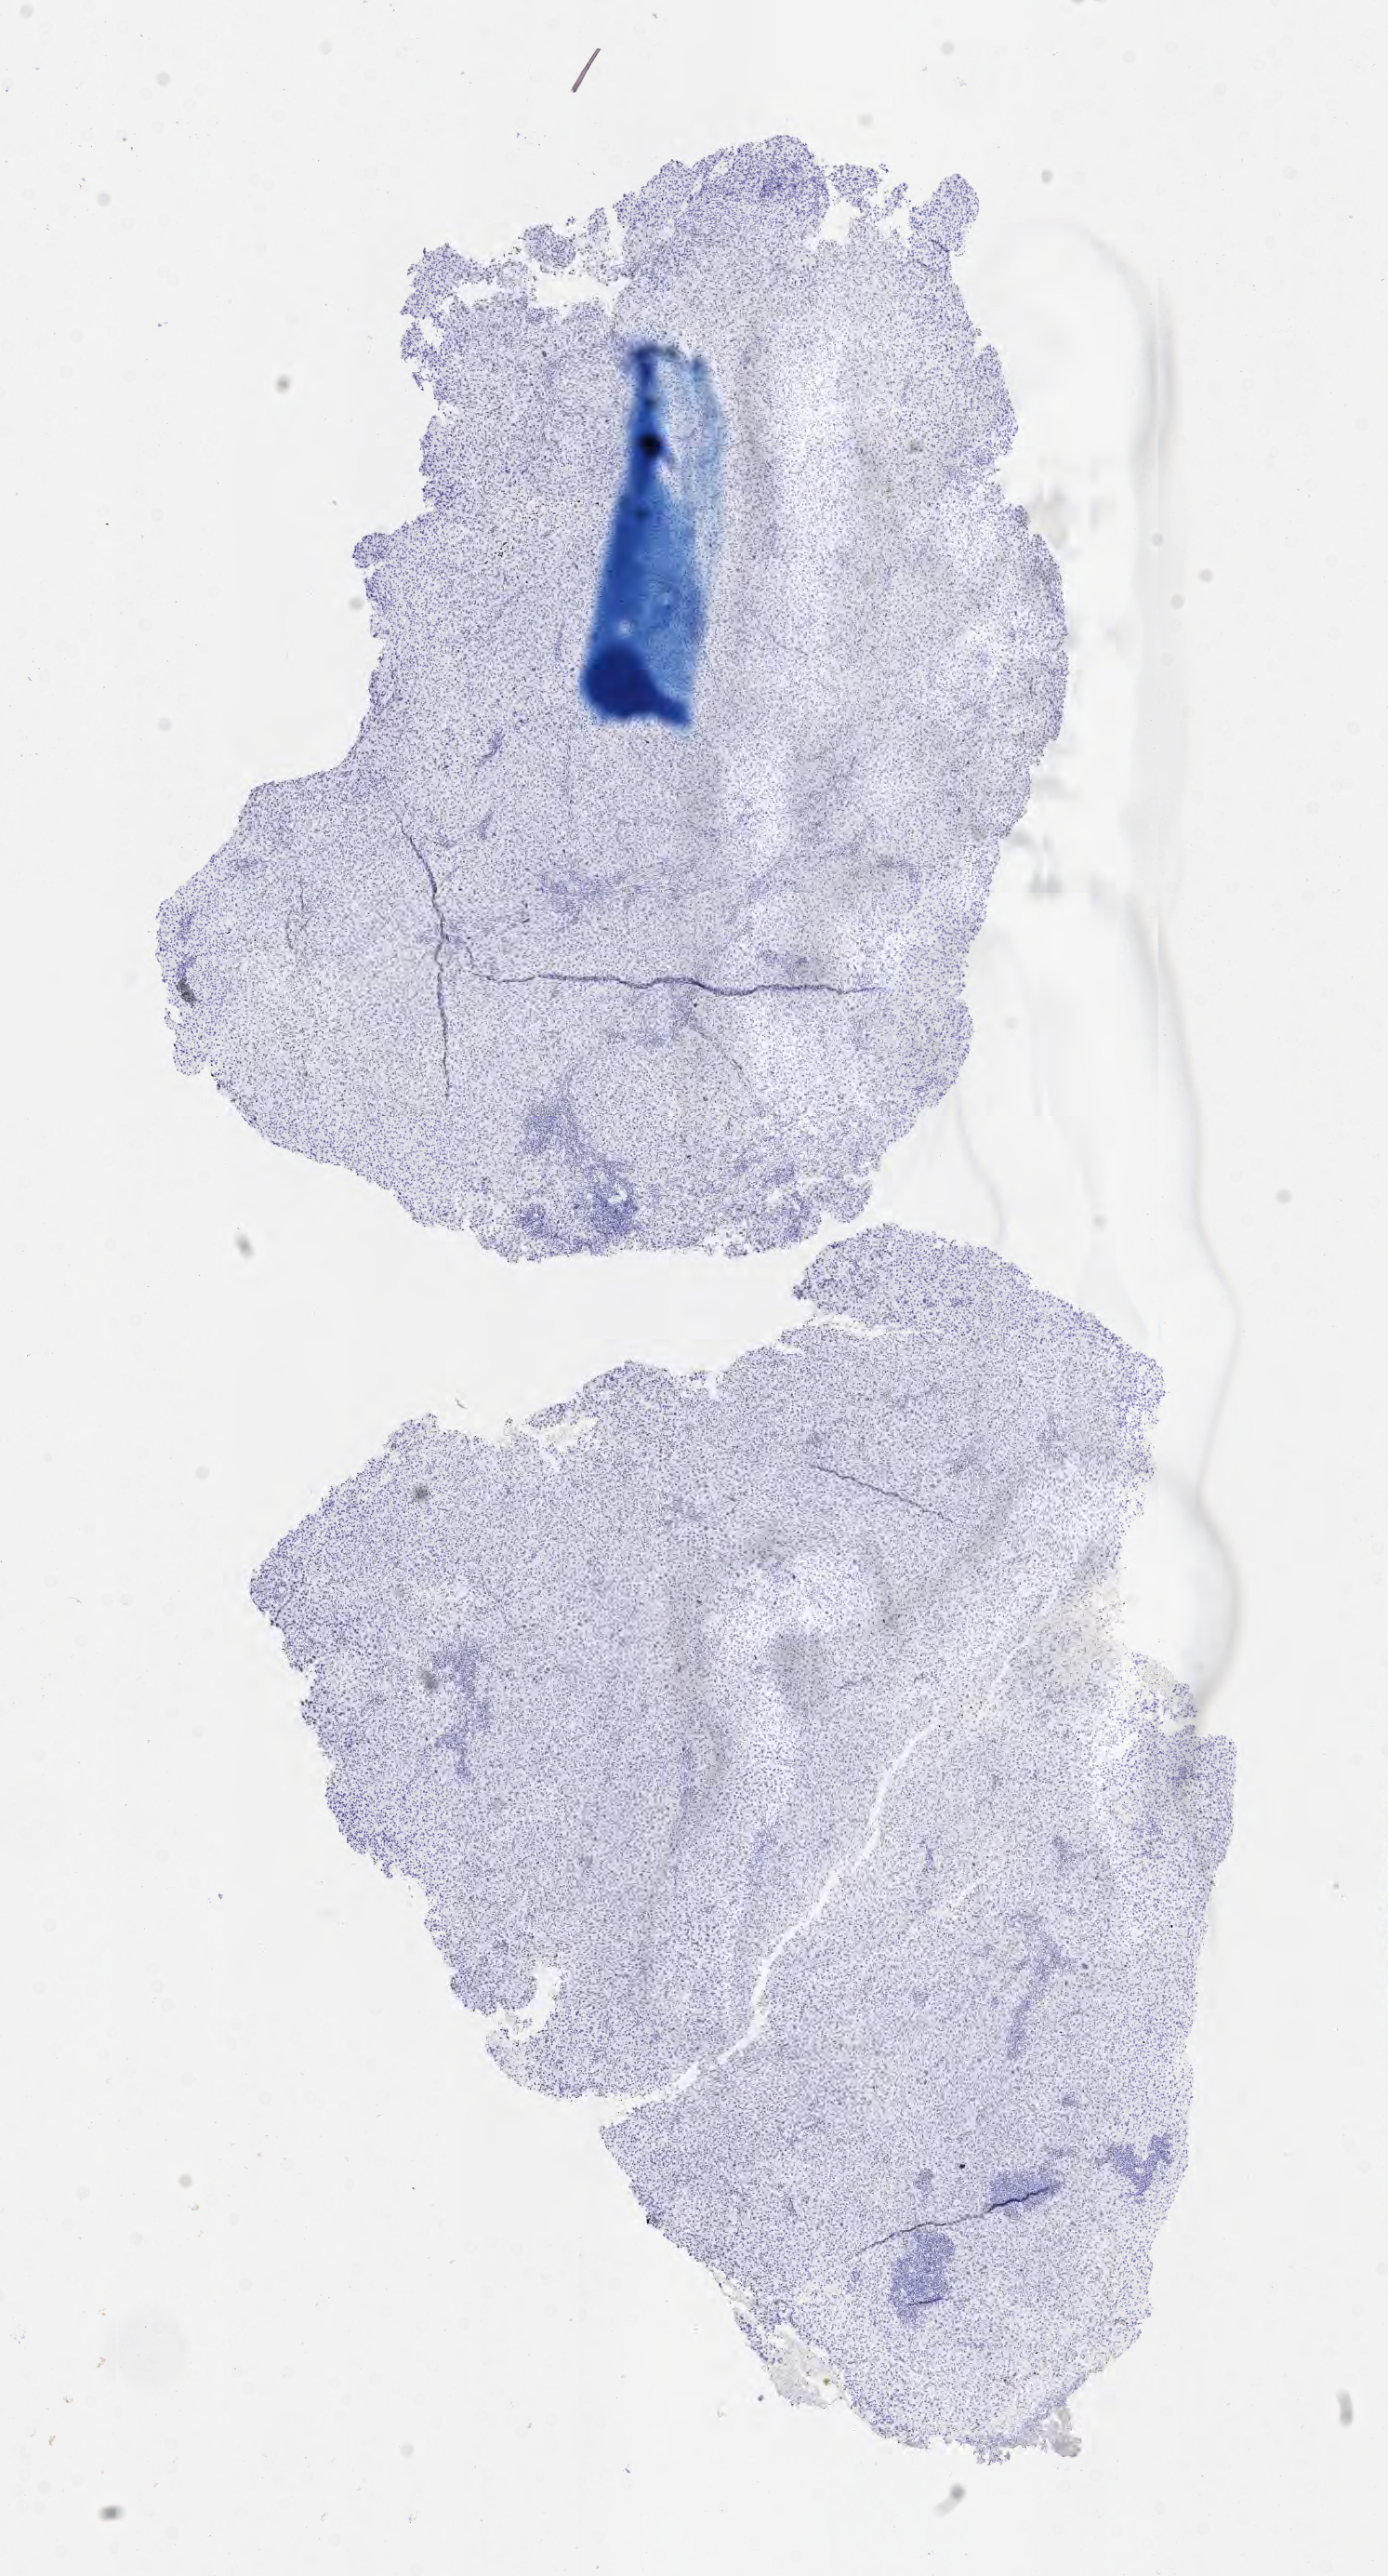
Whole-slide image, immunohistochemical stain for p40, shown as a low-resolution overview of the whole scanned area (about 6.0 x 11.2 mm); tumor tissue; site: cervix. Female patient, 45 years old.
• diagnosis: Squamous cell carcinoma, large cell, nonkeratinizing, NOS